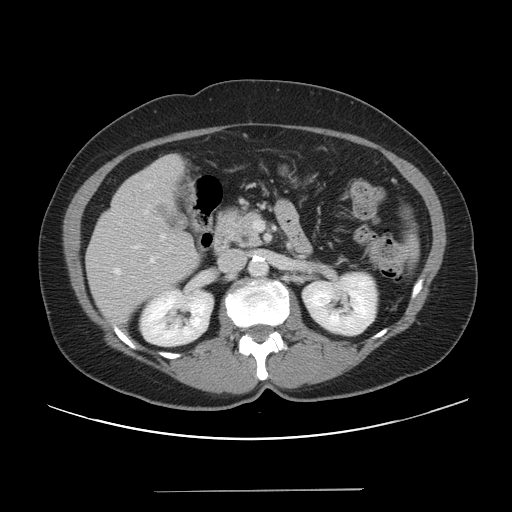
Contrast-enhanced abdominal CT, one axial slice. Position 21 of 56 along the scan axis. Intravenous contrast given. Soft-tissue window (W 400 / L 40 HU). 5 mm slice thickness. 512 × 512 image matrix, field of view 419 × 419 mm. Female patient, age 54 years. From the clinical record (not read from this slice): diagnosis: colorectal cancer liver metastases, imaged before liver resection; multiple liver metastases: yes.
Outlined on this slice (expert manual segmentation):
- hepatic veins: box from (x=115, y=269) to (x=120, y=274) px
- liver: (x=86, y=155)–(x=200, y=327)
- planned liver remnant (the part of the liver to remain after resection): (x=157, y=155)–(x=183, y=181)
- portal vein (with intrahepatic branches): (x=161, y=221)–(x=263, y=239)